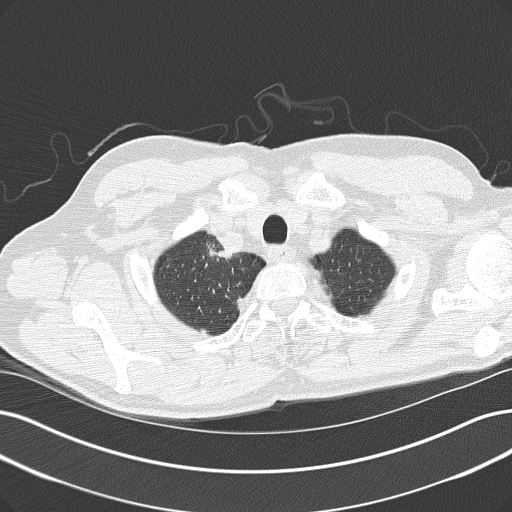
Axial slice from a low-dose chest CT screening exam; baseline screening round; lung window (W 1500 / L -600 HU); 2 mm slice thickness; lung (sharp) reconstruction kernel (B50f). Male participant, aged 61 years at enrolment. Current smoker at enrolment.
Expert-annotated lung lesion, box from (x=194, y=230) to (x=246, y=275) px. The screening reader recorded 2 non-calcified nodules or masses ≥4 mm on this exam; which of them this box marks is not recorded. Participant outcome: lung cancer diagnosed 54 days after this screen — adenocarcinoma, NOS, right upper lobe, poorly differentiated (G3), stage IIIB (AJCC 6th edition).